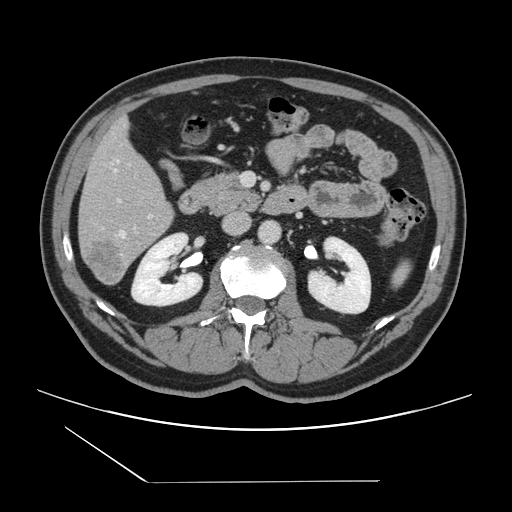
Contrast-enhanced abdominal CT, one axial slice. Position 57 of 157 along the scan axis. 120 kVp. Intravenous contrast given. Soft-tissue window (W 400 / L 40 HU). 2.5 mm slice thickness. 512 × 512 image matrix. Male patient, age 61 years. From the clinical record (not read from this slice): diagnosis: colorectal cancer liver metastases, imaged before liver resection; multiple liver metastases: yes; largest metastasis: 5.5 cm; disease in both lobes: yes.
Outlined on this slice (outlined manually by an expert reader):
- hepatic veins: box from (x=115, y=160) to (x=126, y=237) px
- liver: (x=80, y=121)–(x=174, y=284)
- planned liver remnant (the part of the liver to remain after resection): (x=80, y=121)–(x=168, y=218)
- portal vein (with intrahepatic branches): (x=102, y=199)–(x=152, y=228)
- liver metastasis: (x=85, y=241)–(x=126, y=283)